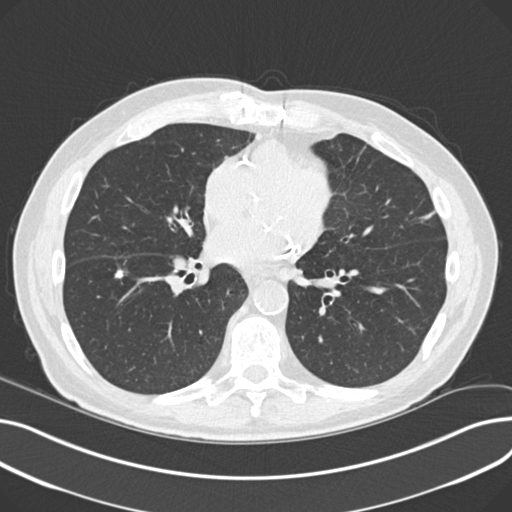
Low-dose screening chest CT, one axial slice. Slice 97 of 230 in the series (ordered by position). Reconstruction kernel B30f. Lung window (W 1500 / L -600 HU). 2 mm slice thickness. 512 × 512 image matrix, field of view 372 × 372 mm.
Structures marked on this image (outlined manually by an expert reader):
- lesion 2 (tumor, lower lobe of right lung): bounding box <114,270,125,279> (left, top, right, bottom; pixels)